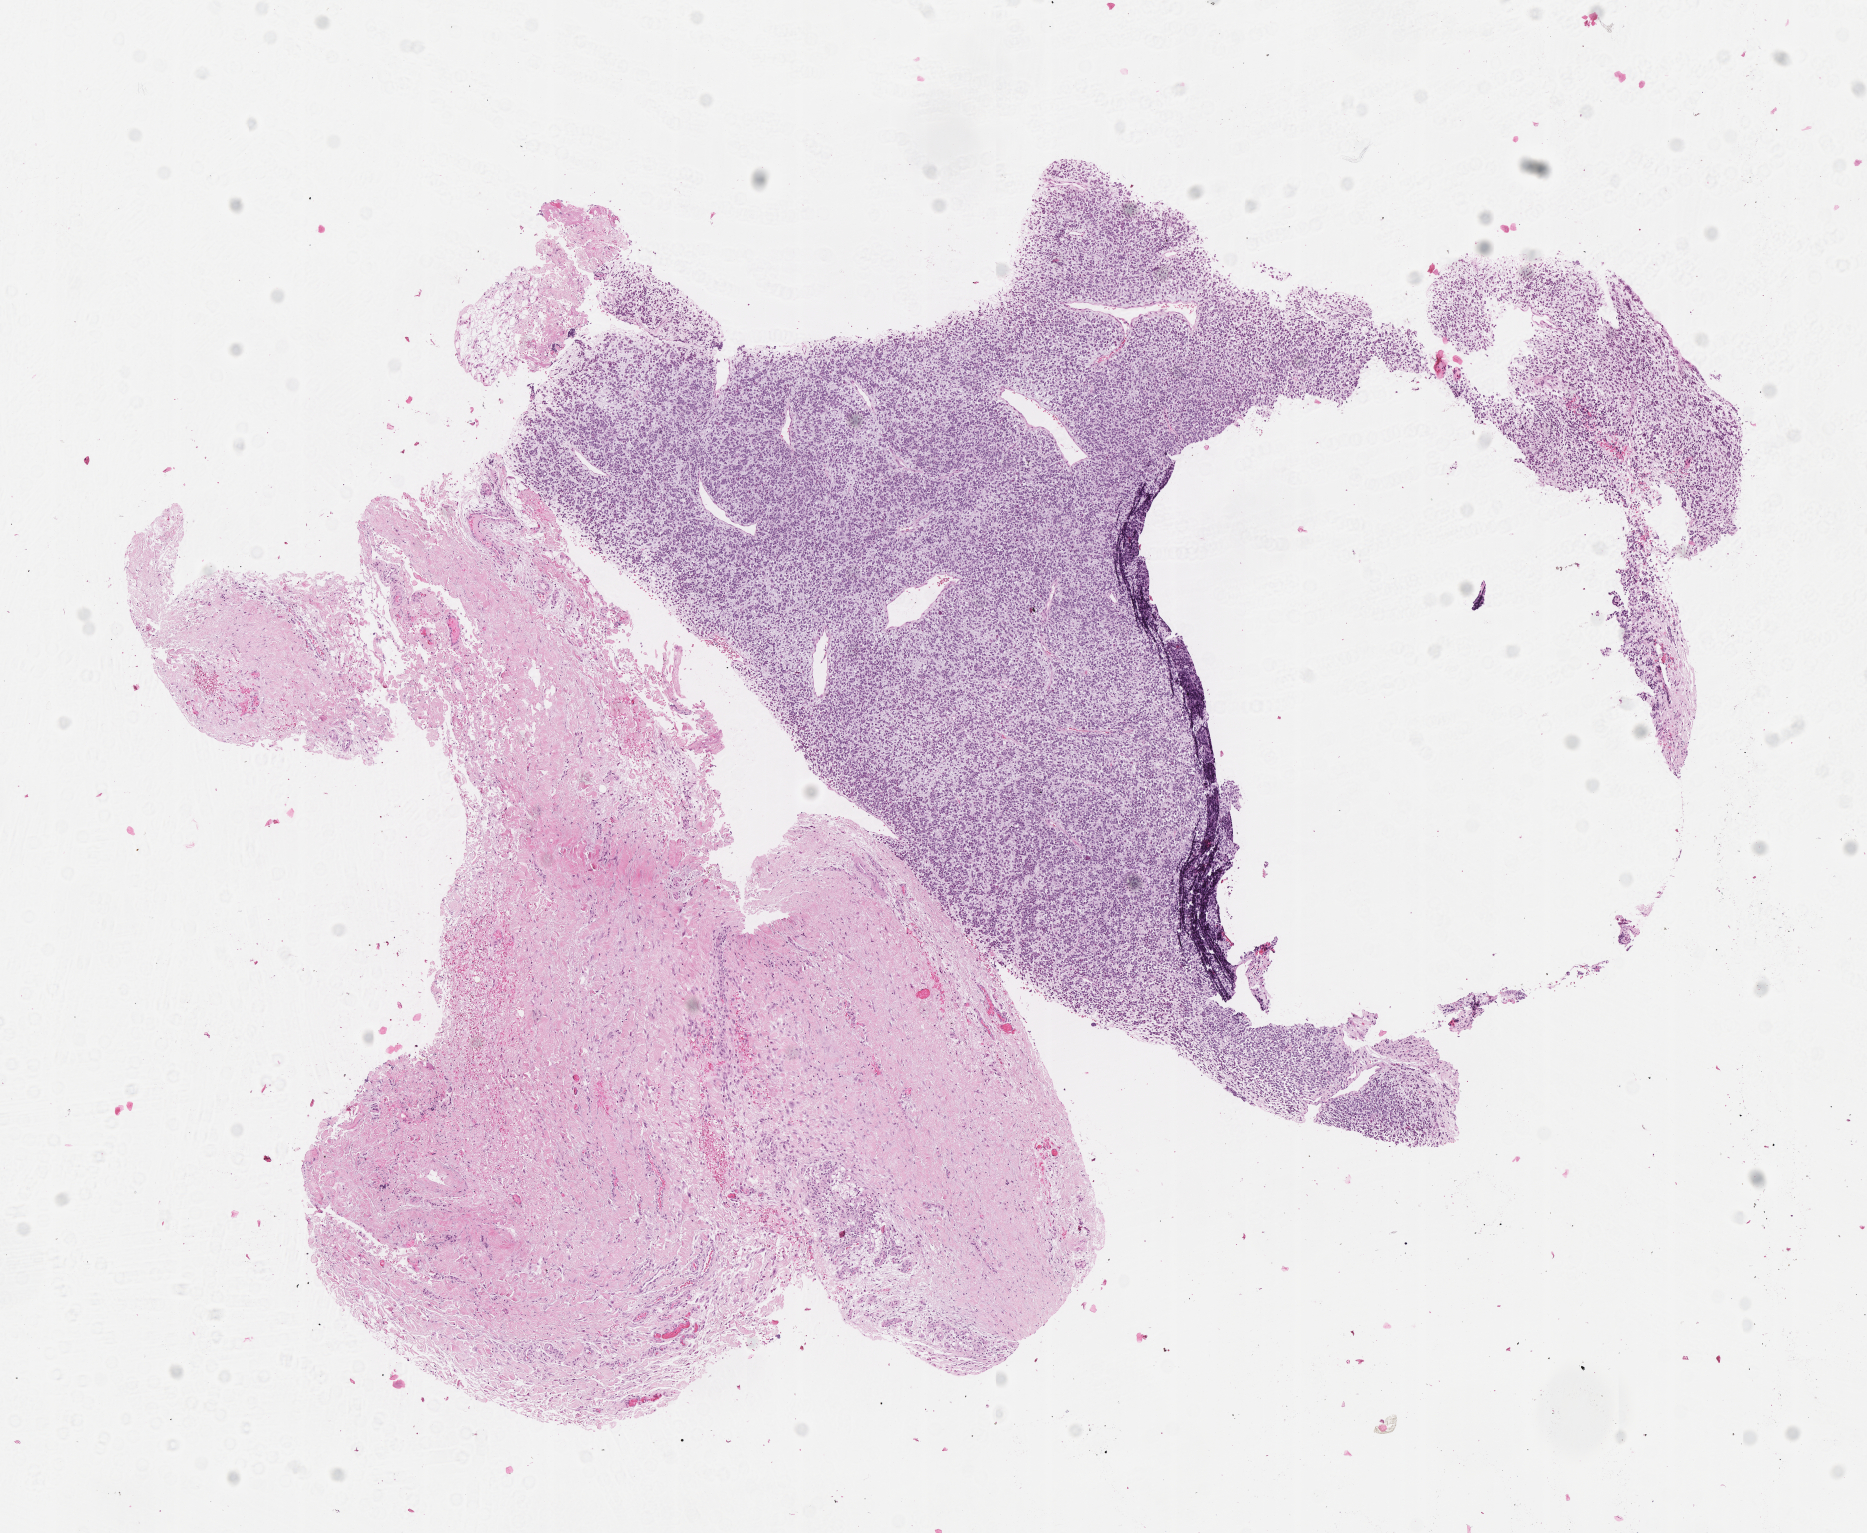
Whole-slide image, H&E stain of tumor tissue — low-resolution overview of the scanned area, about 7.5 x 6.2 mm; FFPE section; sample anatomic site: neck-right. Female patient, age at diagnosis 6.5 years.
* stage (as recorded): 1
* metastatic status at presentation (as recorded): non-metastatic (unconfirmed)
* diagnosis: rhabdomyosarcoma; histological classification: embryonal rhabdomyosarcoma